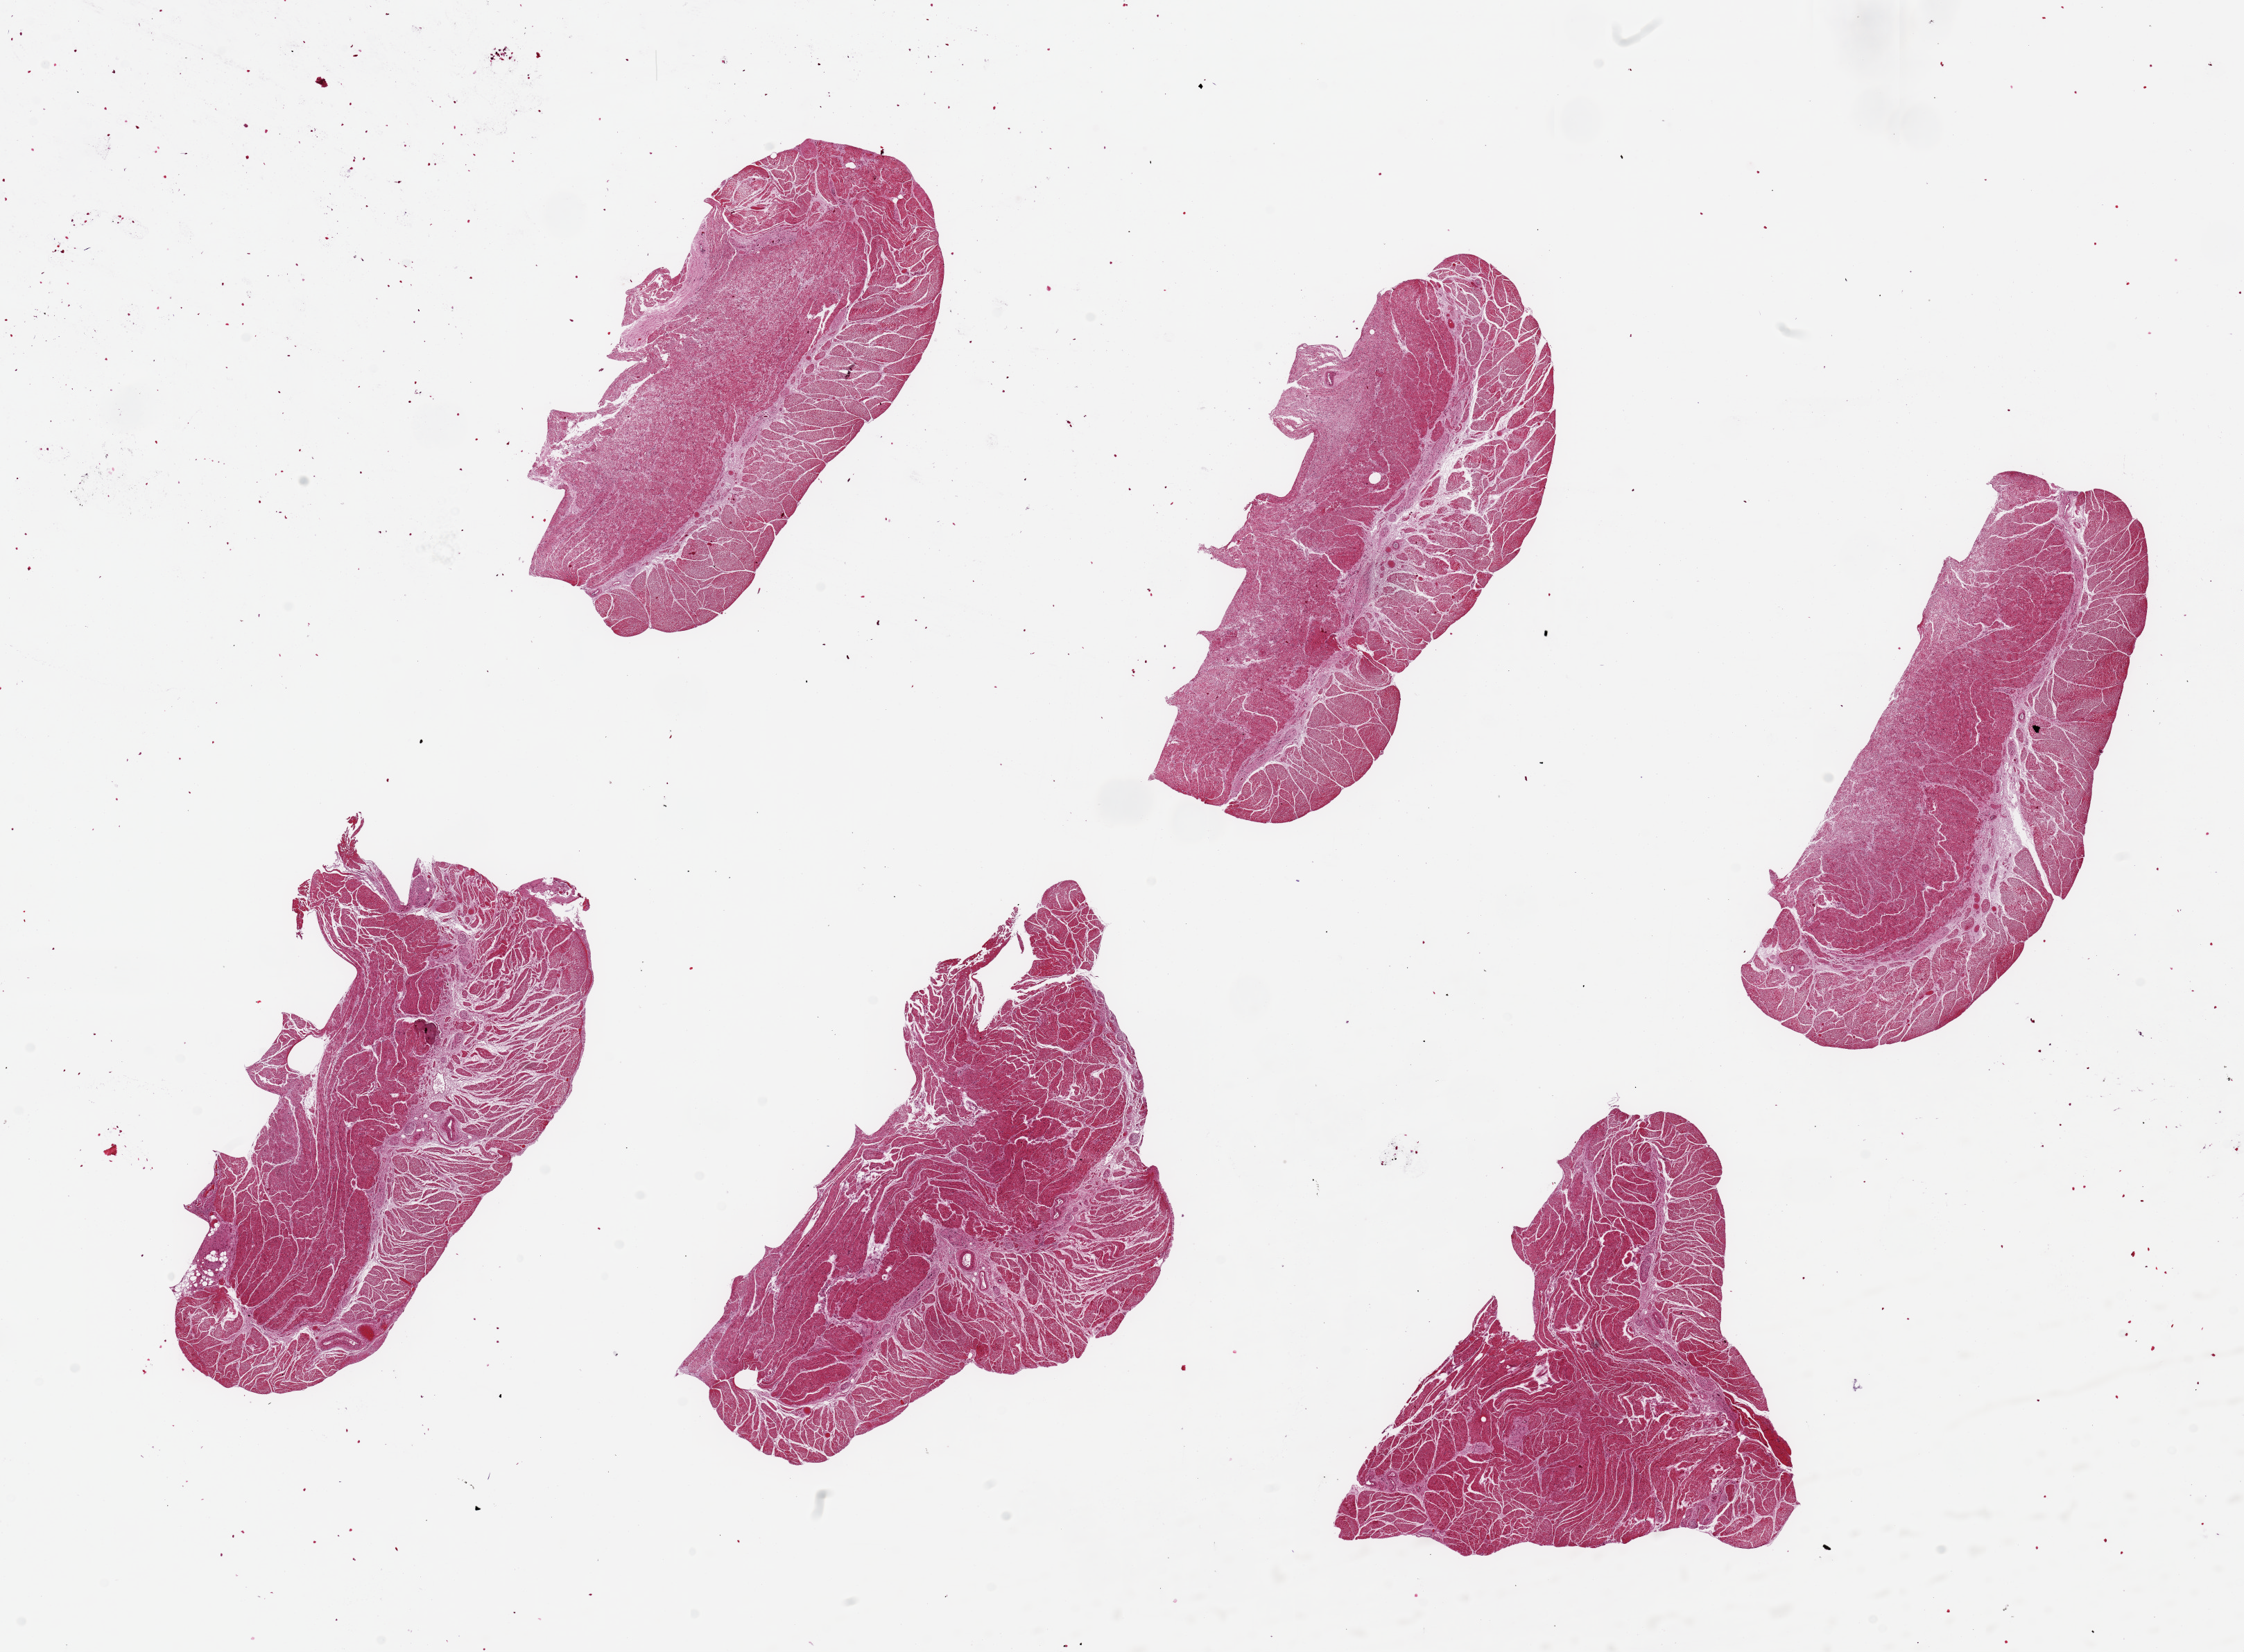
Whole-slide image, H&E stain, whole scanned area (about 25.6 x 18.8 mm, from a 20x scan) shown as a low-resolution overview, PAXgene-fixed, paraffin-embedded tissue, target tissue: esophageal muscle, tissue donor sample. Male donor.
• reviewer comment on this tissue sample: 6 pieces, up to 7x4mm; all muscle